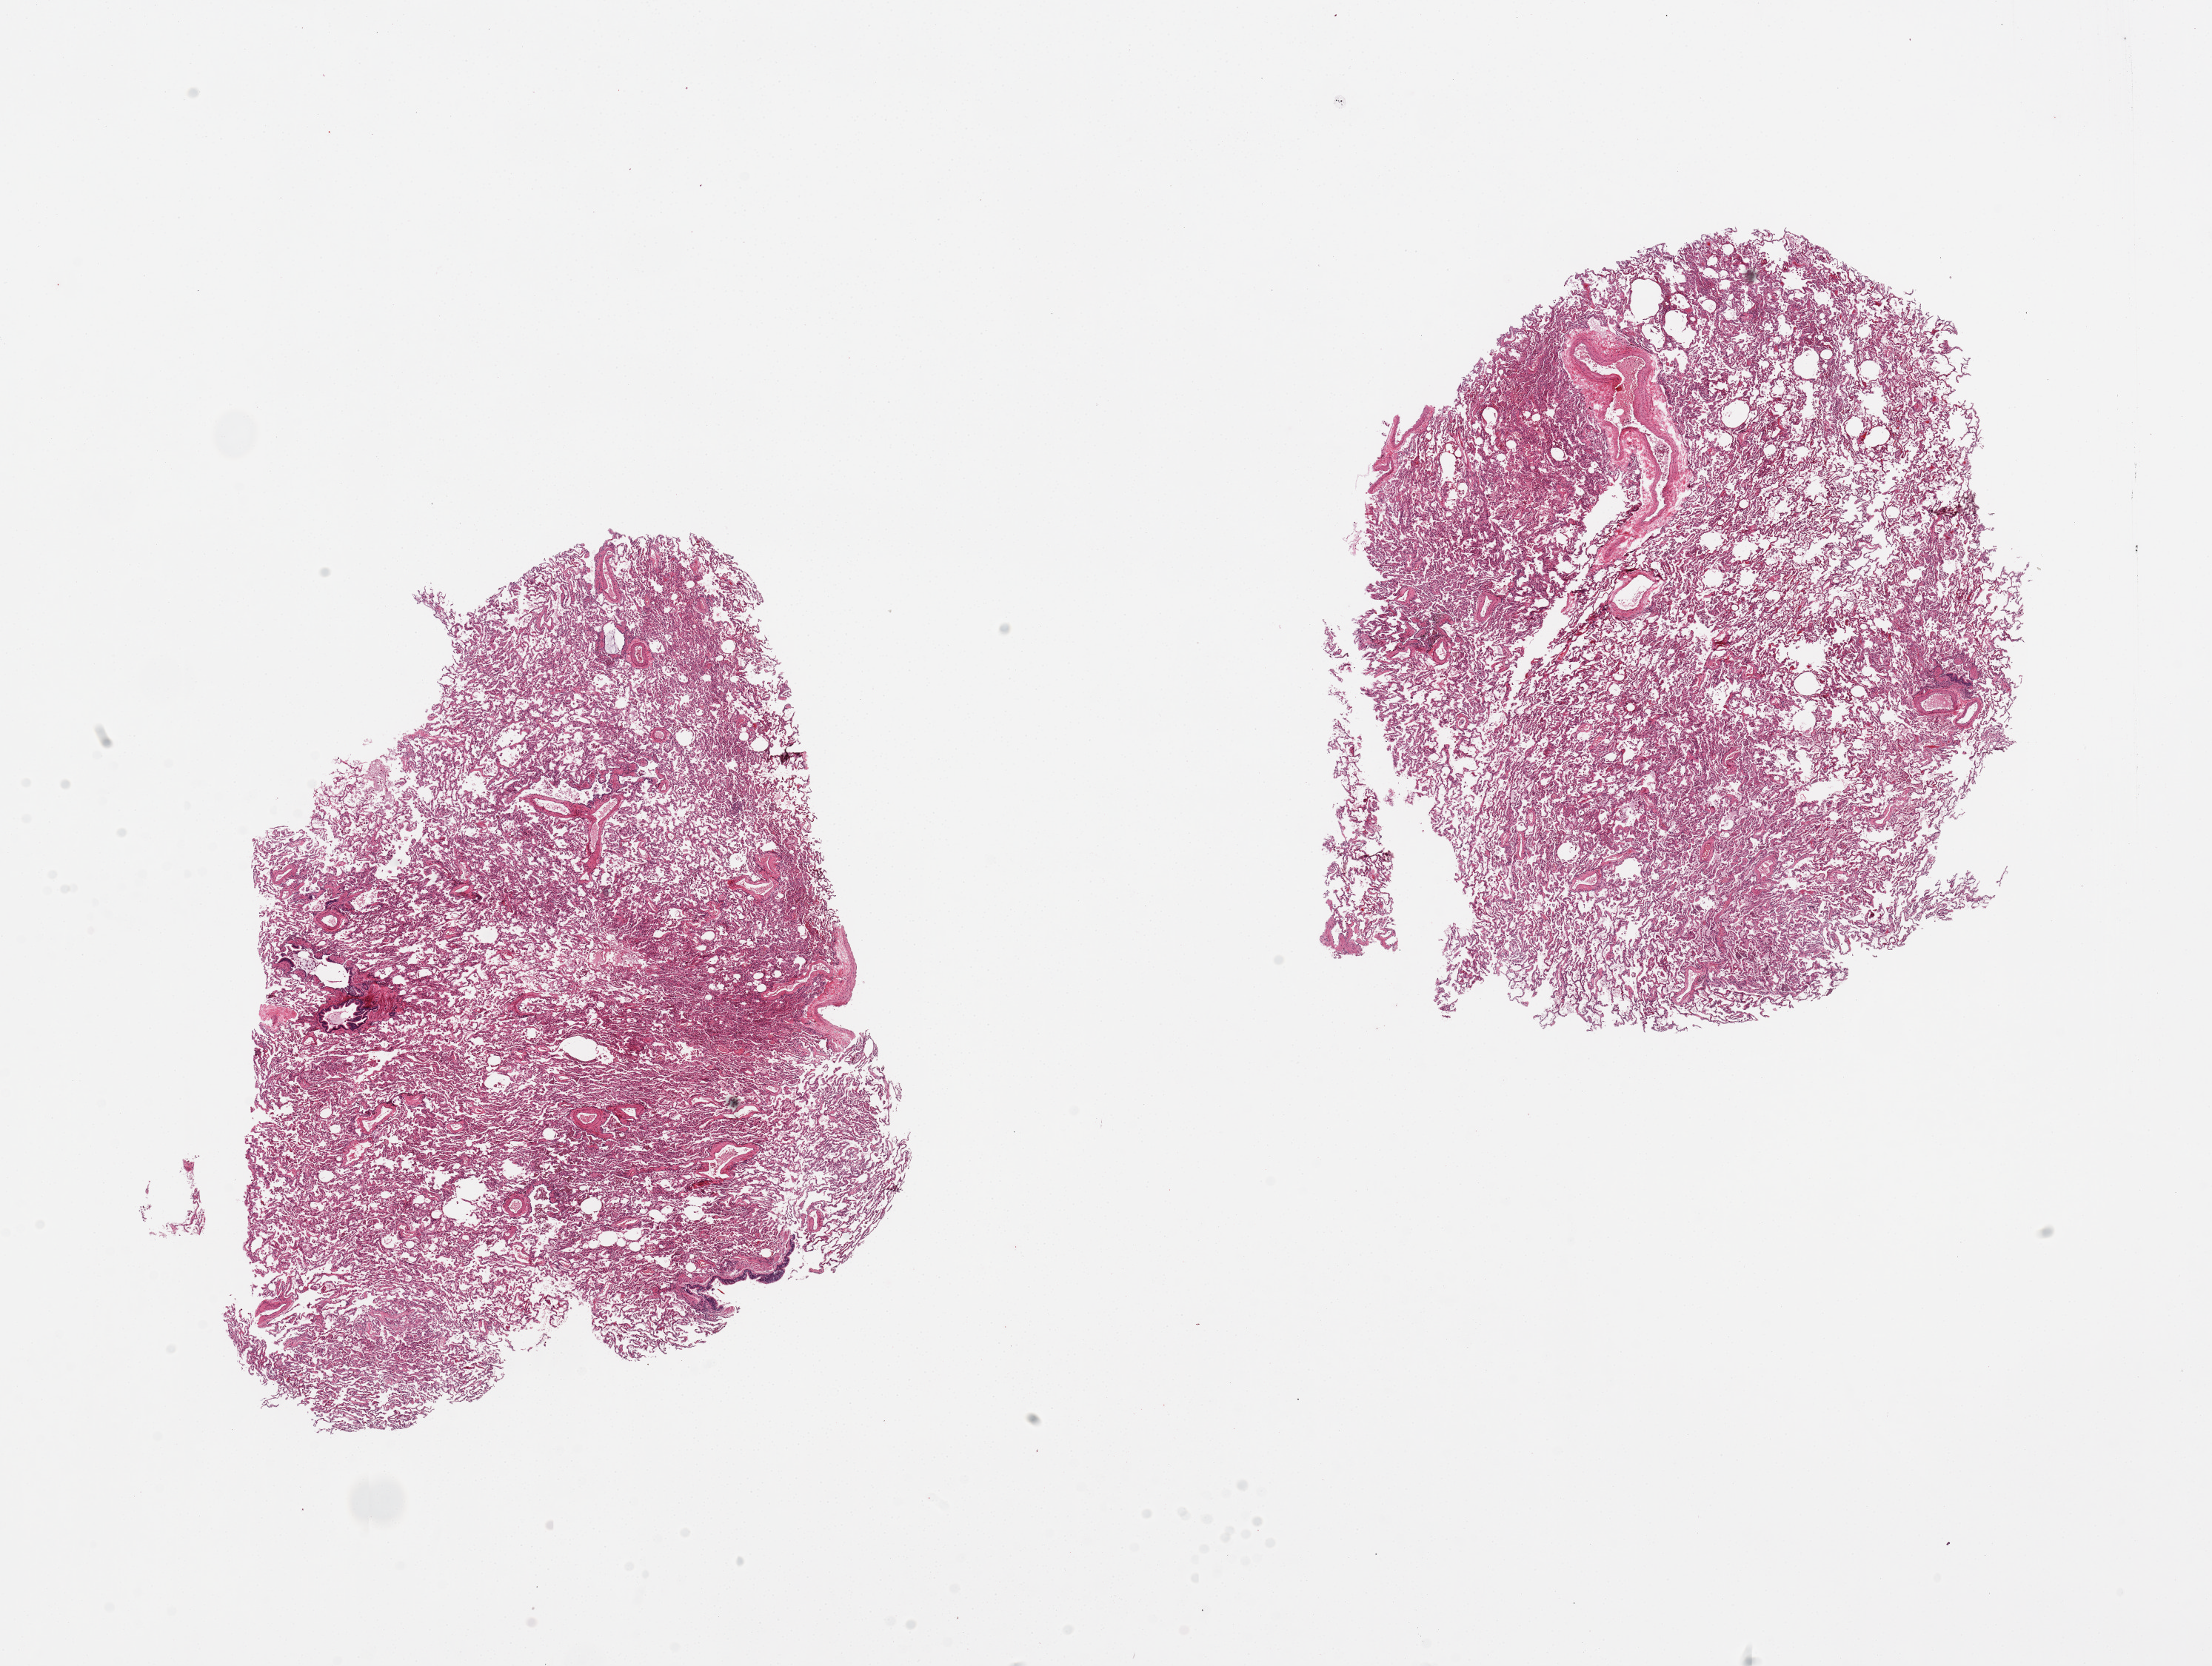
Whole-slide image, hematoxylin and eosin (H&E) stain, a low-resolution overview of the entire scanned area, about 23.6 x 17.8 mm. PAXgene-fixed, paraffin-embedded tissue. Sampled site (target tissue): lung. Tissue donor sample.
Pathologist's review note for this sample: 2 pieces, 9x7 and 8x7mm; moderate congestions, chronic pneumontitis.